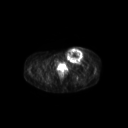
FDG PET of an extremity soft-tissue mass (from a PET/CT study), one axial slice; slice 64 of 267 in the series (ordered by position); 3.27 mm slice thickness; 128 × 128 image matrix, field of view 600 × 600 mm. Patient: female, 24 years. From the clinical record (not read from this slice): histological type: leiomyosarcoma; grade: high; site of the primary tumour: groin.
Outlined on this slice (expert contour drawn on MRI and transferred to this co-registered scan by the dataset authors):
- gross tumour volume including surrounding oedema: bounding box [x1, y1, x2, y2] px = [65, 46, 91, 64]
- gross tumour volume (mass): [65, 48, 84, 64]